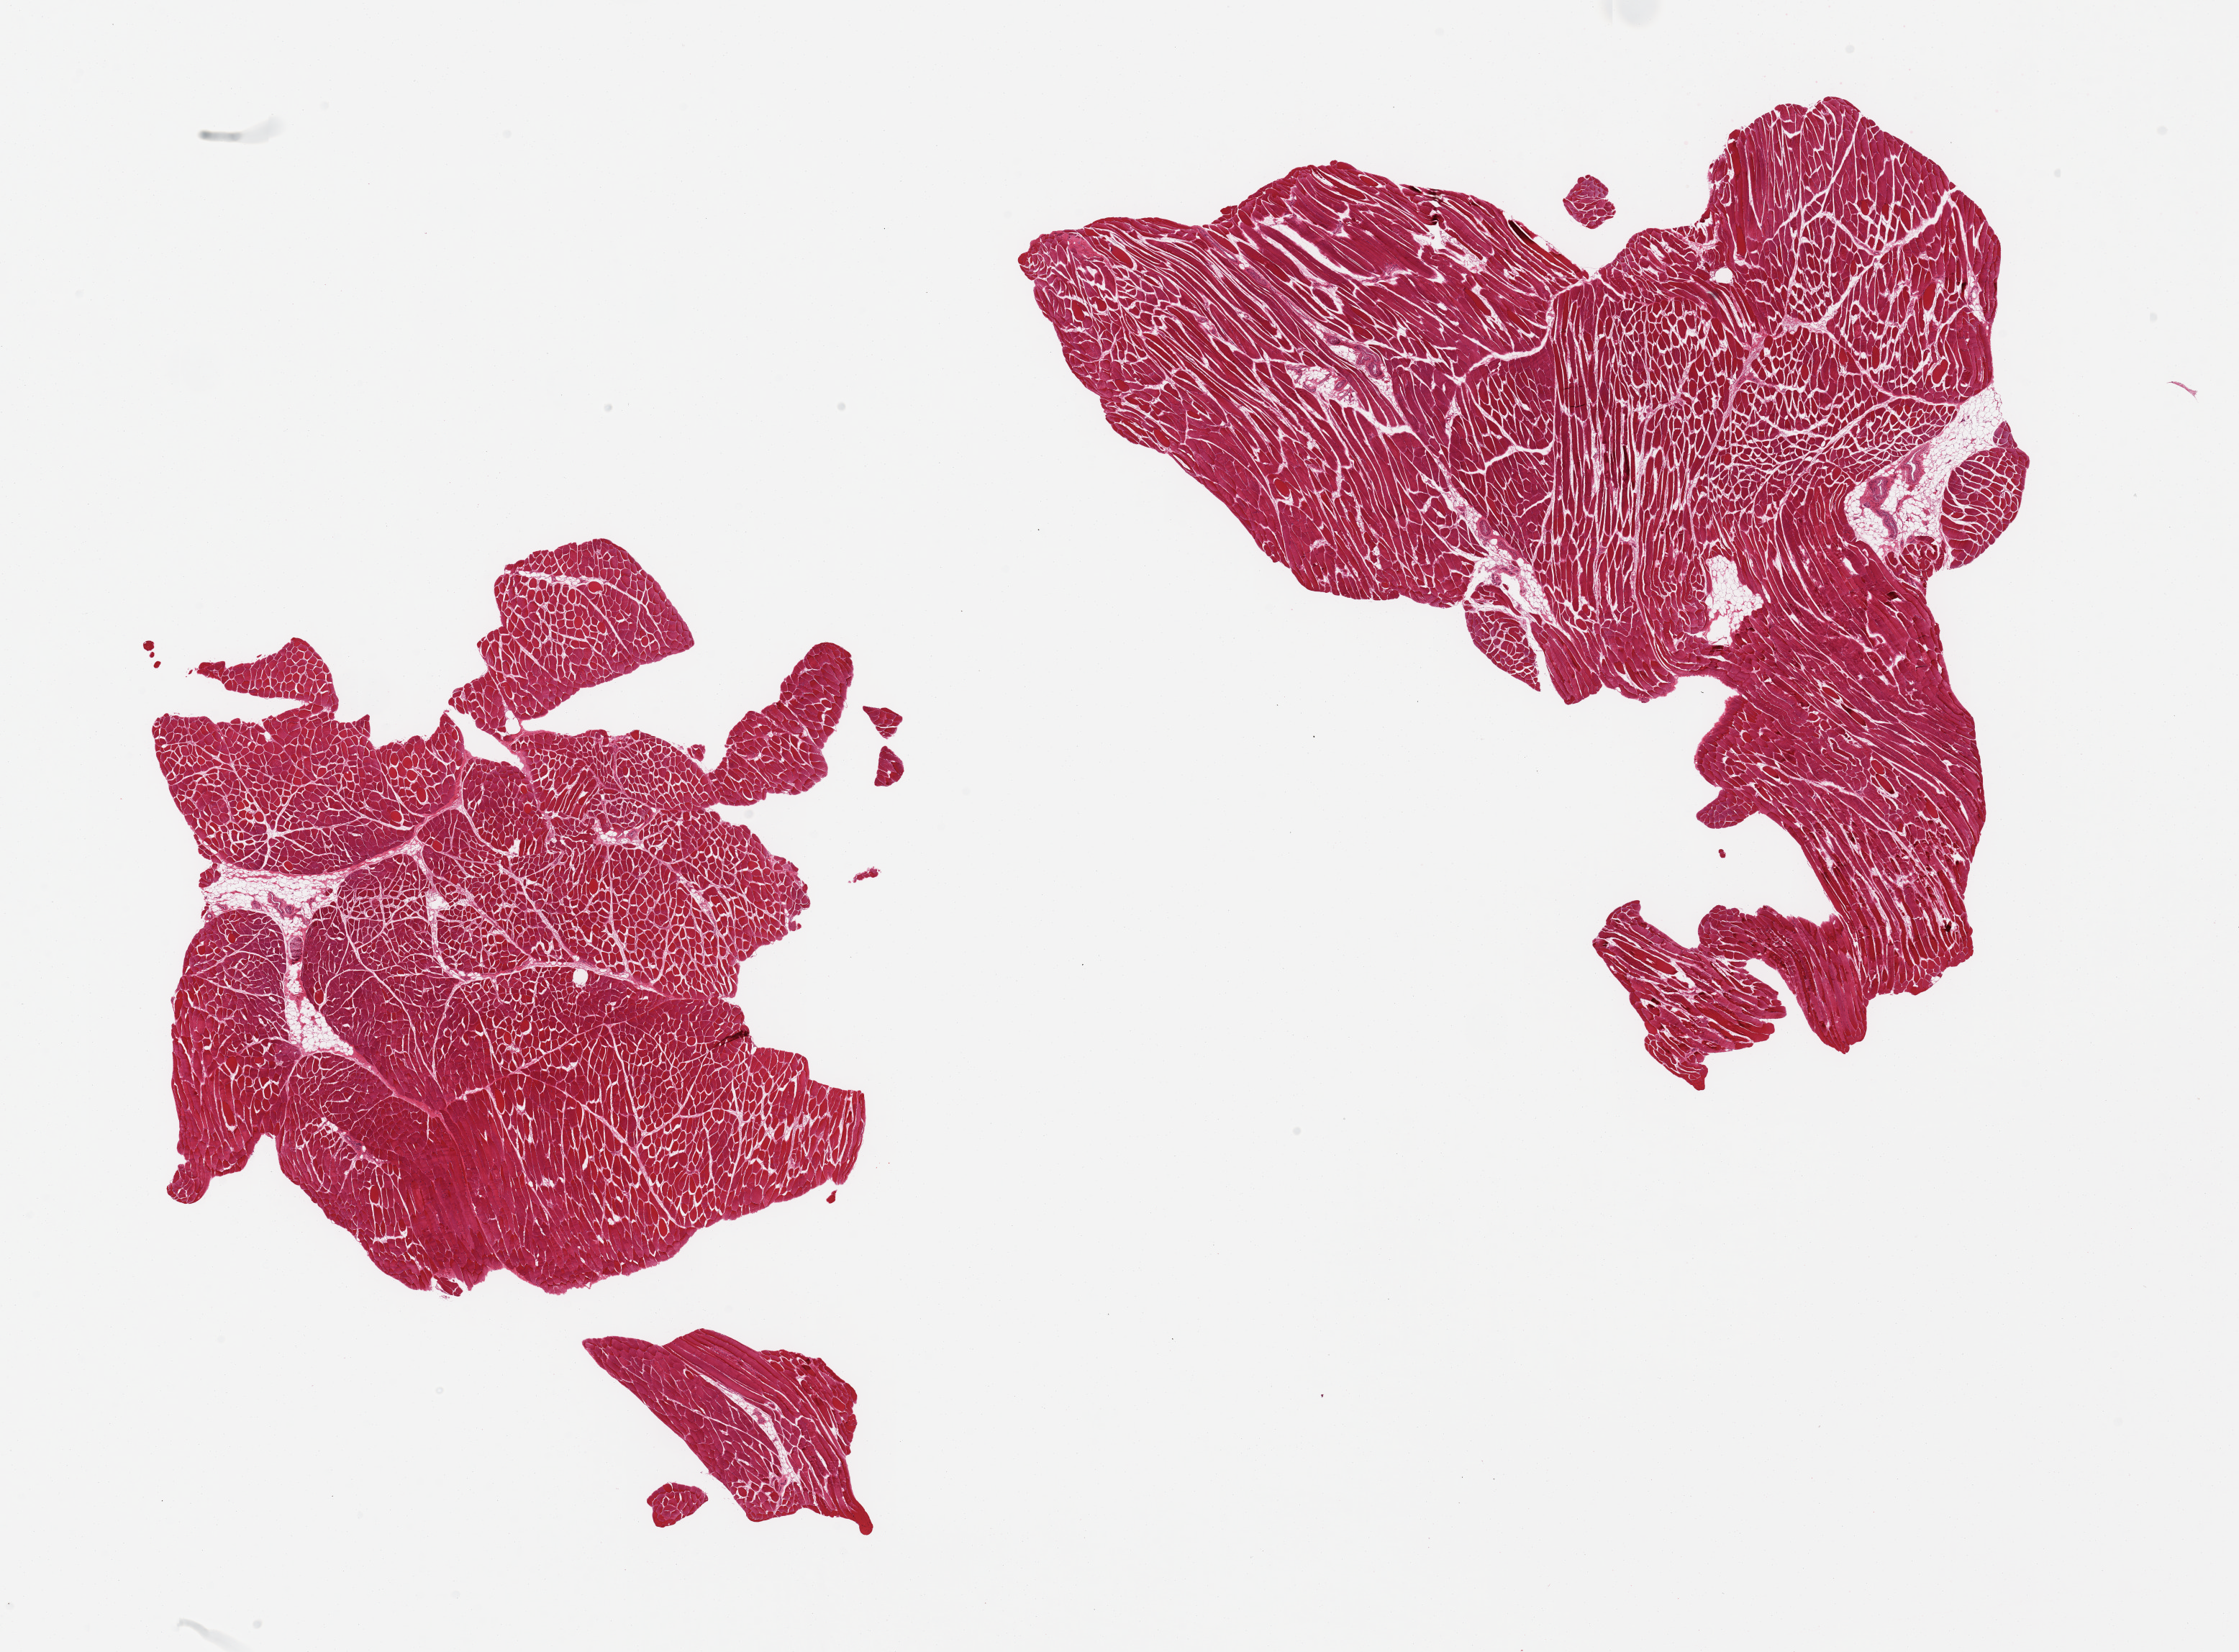
Digitized haematoxylin and eosin-stained section, low-resolution overview of the scanned area, about 24.6 x 18.2 mm. PAXgene-fixed paraffin-embedded (PFPE) section. Target tissue: skeletal muscle. Tissue donor sample. Female donor.
Review note (as recorded): 2 pieces; well trimmed.